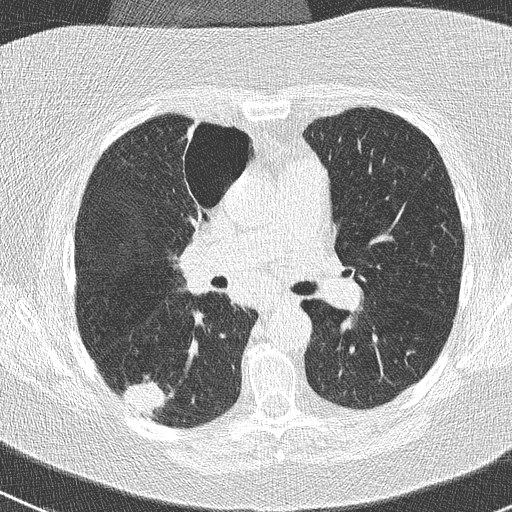
Low-dose screening chest CT, one axial slice; position 152 of 261 along the scan axis; reconstruction kernel B50f; 120 kVp; lung window (W 1500 / L -600 HU); 2 mm slice thickness; 512 × 512 image matrix.
Structures marked on this image (expert manual segmentation):
- lesion 1 (tumor, lower lobe of right lung): bounding box [x1, y1, x2, y2] px = [123, 381, 166, 419]